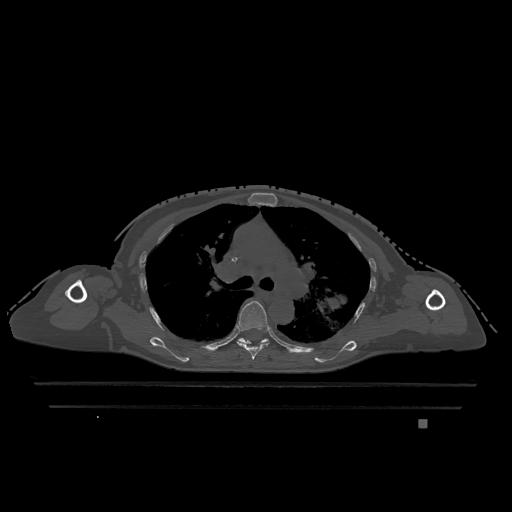
CT including the spine, one axial slice; position 822 of 1317 along the scan axis; bone window (W 1800 / L 400 HU); 0.5 mm slice thickness; 512 × 512 image matrix, field of view 500 × 500 mm. Patient: female, 74 years. Case-level facts recorded for this patient, not image findings: primary cancer: lung; vertebrae with lytic lesions (as recorded): T1, T4, T5, T6, L4, L5.
Structures marked on this image (semi-automatic segmentation, software-assisted and operator-edited):
- T5 vertebra: bounding box <237,301,270,360> (left, top, right, bottom; pixels)
- T6 vertebra: <238,338,269,344>